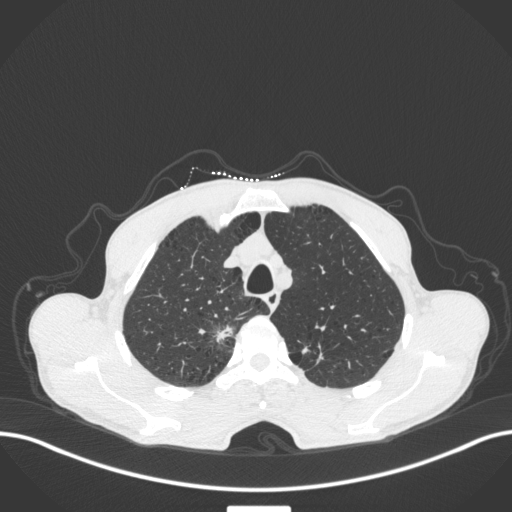
Chest CT, one axial slice; slice 349 of 445 in the series (ordered by position); reconstruction kernel B31f; 120 kVp; lung window (W 1500 / L -600 HU); 1 mm slice thickness; 512 × 512 image matrix, field of view 400 × 400 mm. Male patient, age 70 years. From the clinical record (not read from this slice): clinical TNM (as recorded): T1a N0 M0; histopathological grade: G1-2.
Outlined on this slice (rectangle marked by the reading radiologist):
- lung tumour (recorded histology: adenocarcinoma): bounding box (x1, y1, x2, y2) in pixels: (194, 318, 234, 347)